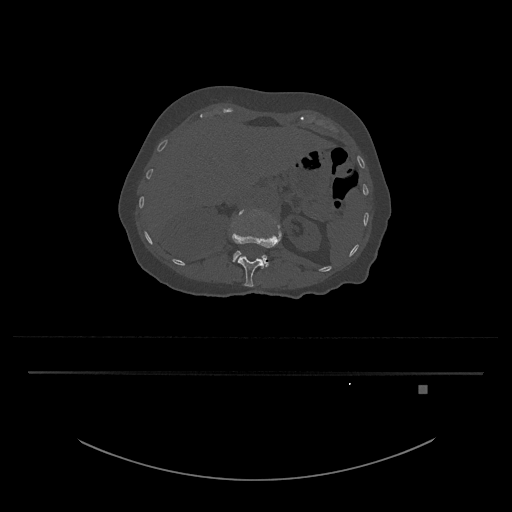
CT including the spine, one axial slice. Position 535 of 797 along the scan axis. Reconstruction kernel Br40s/3. 120 kVp. Bone window (W 1800 / L 400 HU). 0.5 mm slice thickness. 512 × 512 image matrix, field of view 500 × 500 mm. Patient: female, 57 years. From the clinical record (not read from this slice): primary cancer: cervical.
Outlined on this slice (semi-automatically segmented with operator editing):
- L1 vertebra: bounding box [x1, y1, x2, y2] px = [232, 222, 282, 287]